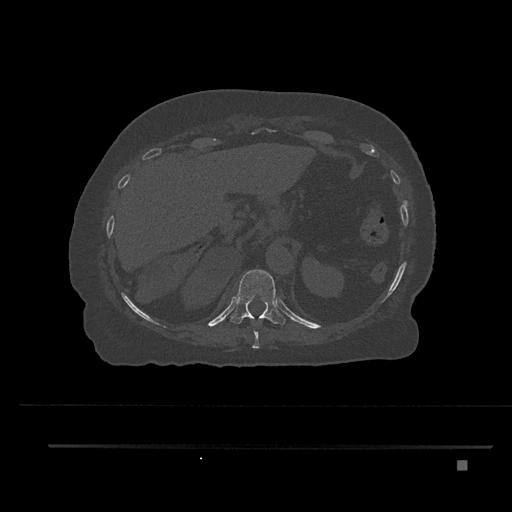
CT including the spine, one axial slice. Reconstruction kernel Br40s/3. 120 kVp. Bone window (W 1800 / L 400 HU). 0.5 mm slice thickness. 512 × 512 image matrix, field of view 437 × 437 mm. Patient: female, 76 years. Case-level facts recorded for this patient, not image findings: primary cancer: lung; vertebrae with lytic lesions (as recorded): T11, L3.
Annotated regions visible in this slice (semi-automatic segmentation, software-assisted and operator-edited):
- T10 vertebra: box from (x=252, y=319) to (x=260, y=349) px
- T11 vertebra: (x=230, y=269)–(x=286, y=325)